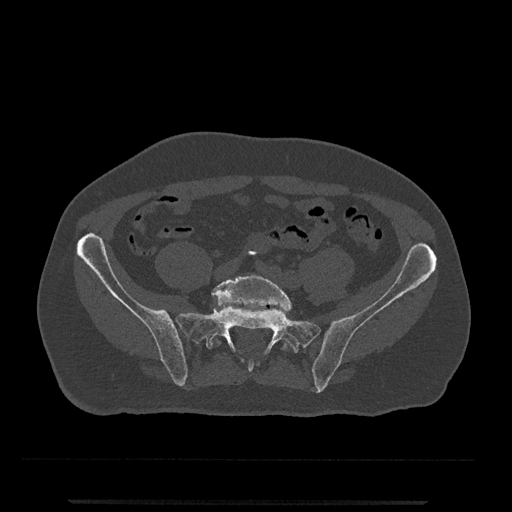
CT including the spine, one axial slice. Position 34 of 797 along the scan axis. 120 kVp. Bone window (W 1800 / L 400 HU). 0.5 mm slice thickness. 512 × 512 image matrix, field of view 419 × 419 mm. Patient: male, 63 years. Case-level facts recorded for this patient, not image findings: primary cancer: prostate.
Outlined on this slice (semi-automatically segmented with operator editing):
- L5 vertebra: bounding box (x1, y1, x2, y2) in pixels: (212, 274, 292, 351)